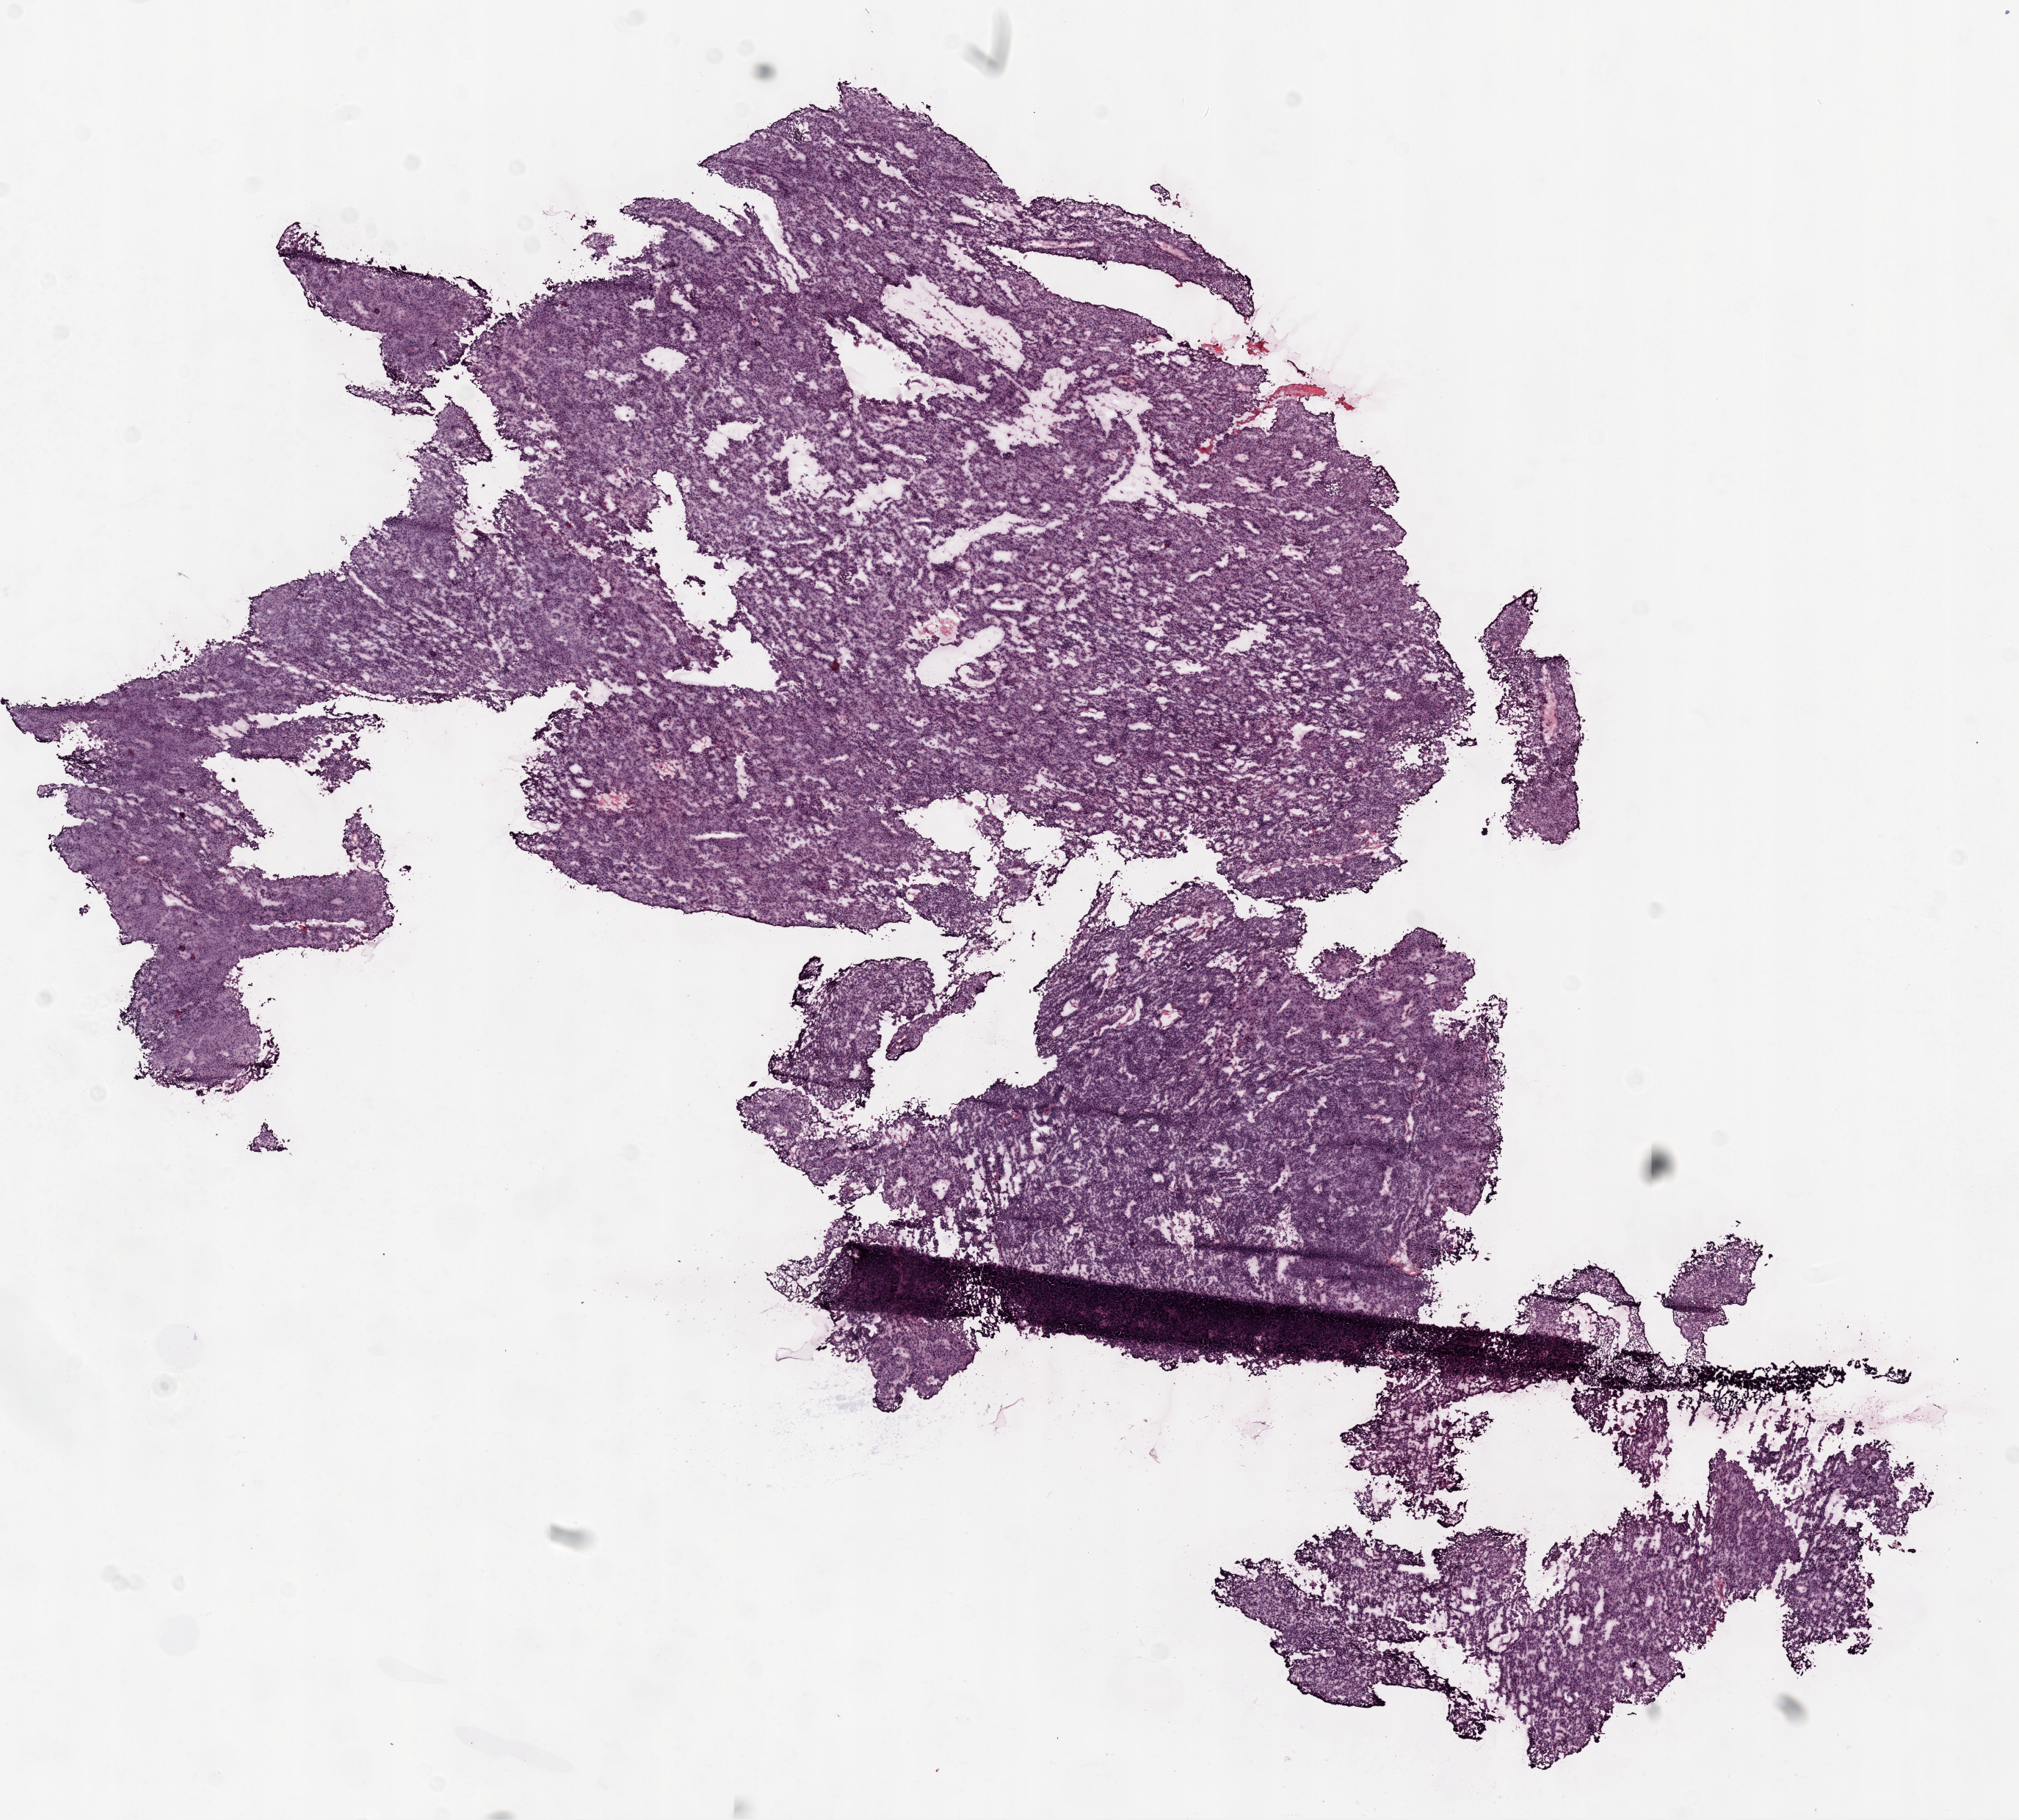
Whole-slide histology image, Hematoxylin and eosin (H&E) stained, whole scanned area (about 11.0 x 9.9 mm) shown as a low-resolution overview; frozen section from the top of the tissue portion; primary tumour sample from the ovary. Female, age 62 years at initial diagnosis.
Histologic diagnosis: Serous cystadenocarcinoma, NOS.